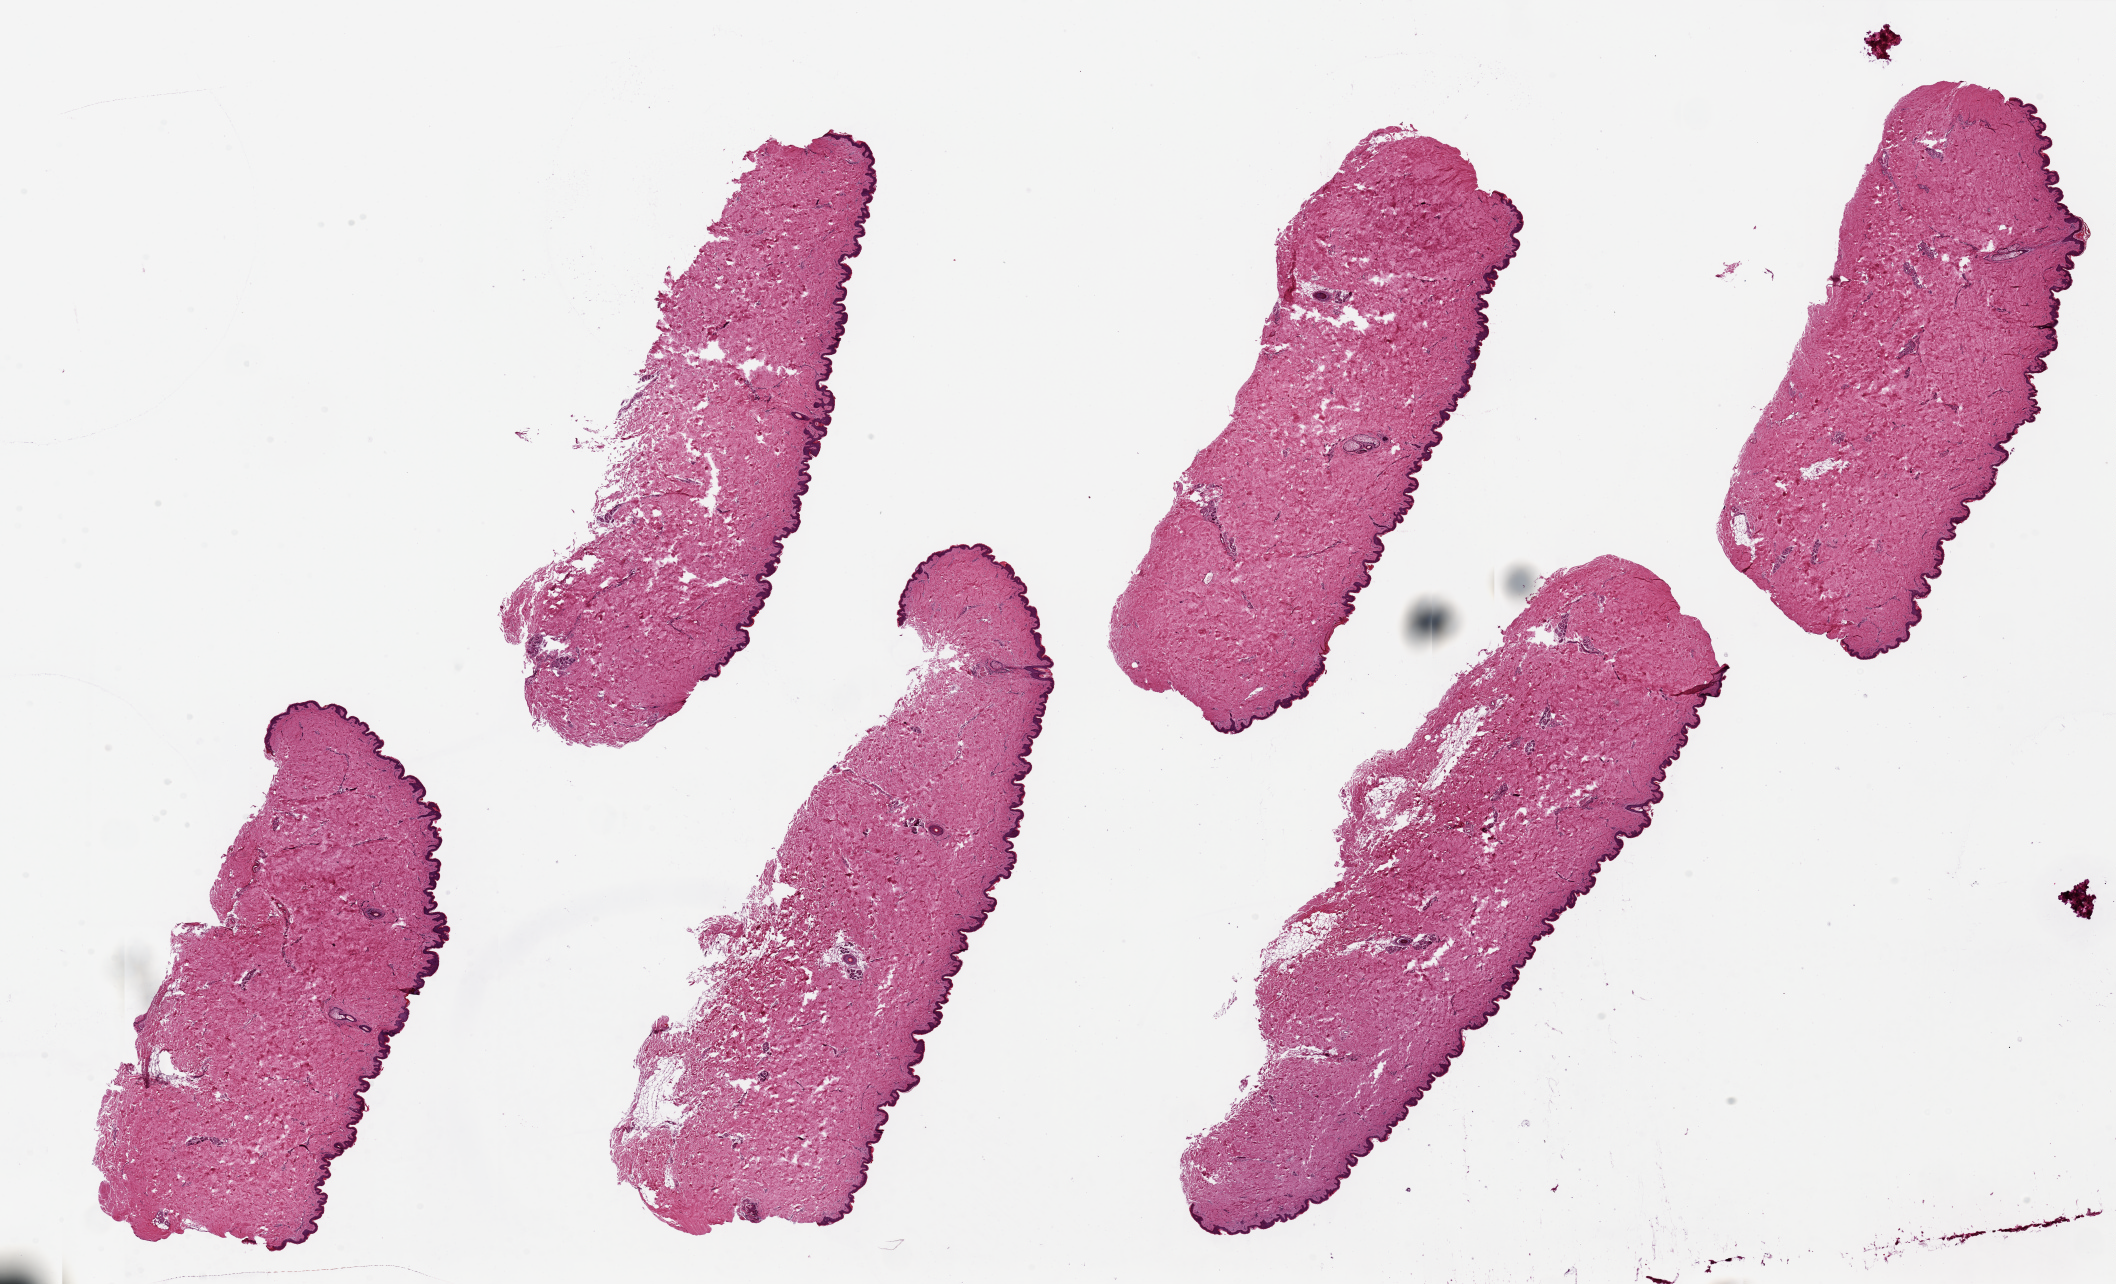
Digitized haematoxylin and eosin-stained section — shown as a low-resolution overview of the whole scanned area (about 33.5 x 20.3 mm, slide scanned at 20x). PAXgene-fixed paraffin-embedded (PFPE) section. Target tissue: skin of suprapubic region. Tissue donor sample. Female donor.
* pathologist's review note for this sample: 6 pieces, up to 12.5x4mm; well trimmed without subcutaneous adipose